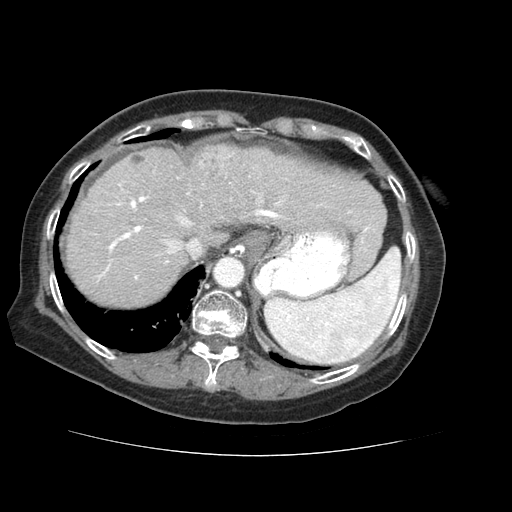
Contrast-enhanced abdominal CT (liver protocol), one axial slice. Position 50 of 73 along the scan axis. Reconstruction kernel STANDARD. 120 kVp. Soft-tissue window (W 400 / L 40 HU). 2.5 mm slice thickness. 512 × 512 image matrix. From the clinical record (not read from this slice): diagnosis: hepatocellular carcinoma (patient treated with transarterial chemoembolisation; whether this scan precedes or follows treatment is not stated here); TNM stage (as recorded): Stage-IVB; Child-Pugh class: A; tumour differentiation: well differentiated; tumour nodularity: uninodular.
Annotated regions visible in this slice (semi-automatically segmented with operator editing):
- abdominal aorta: bounding box <215,258,244,286> (left, top, right, bottom; pixels)
- liver parenchyma outside the tumour (the mass and vessels are separate outlines, so this box may not span the whole liver): <66,144,383,306>
- mass: <195,145,234,186>
- liver vessels: <97,177,352,279>